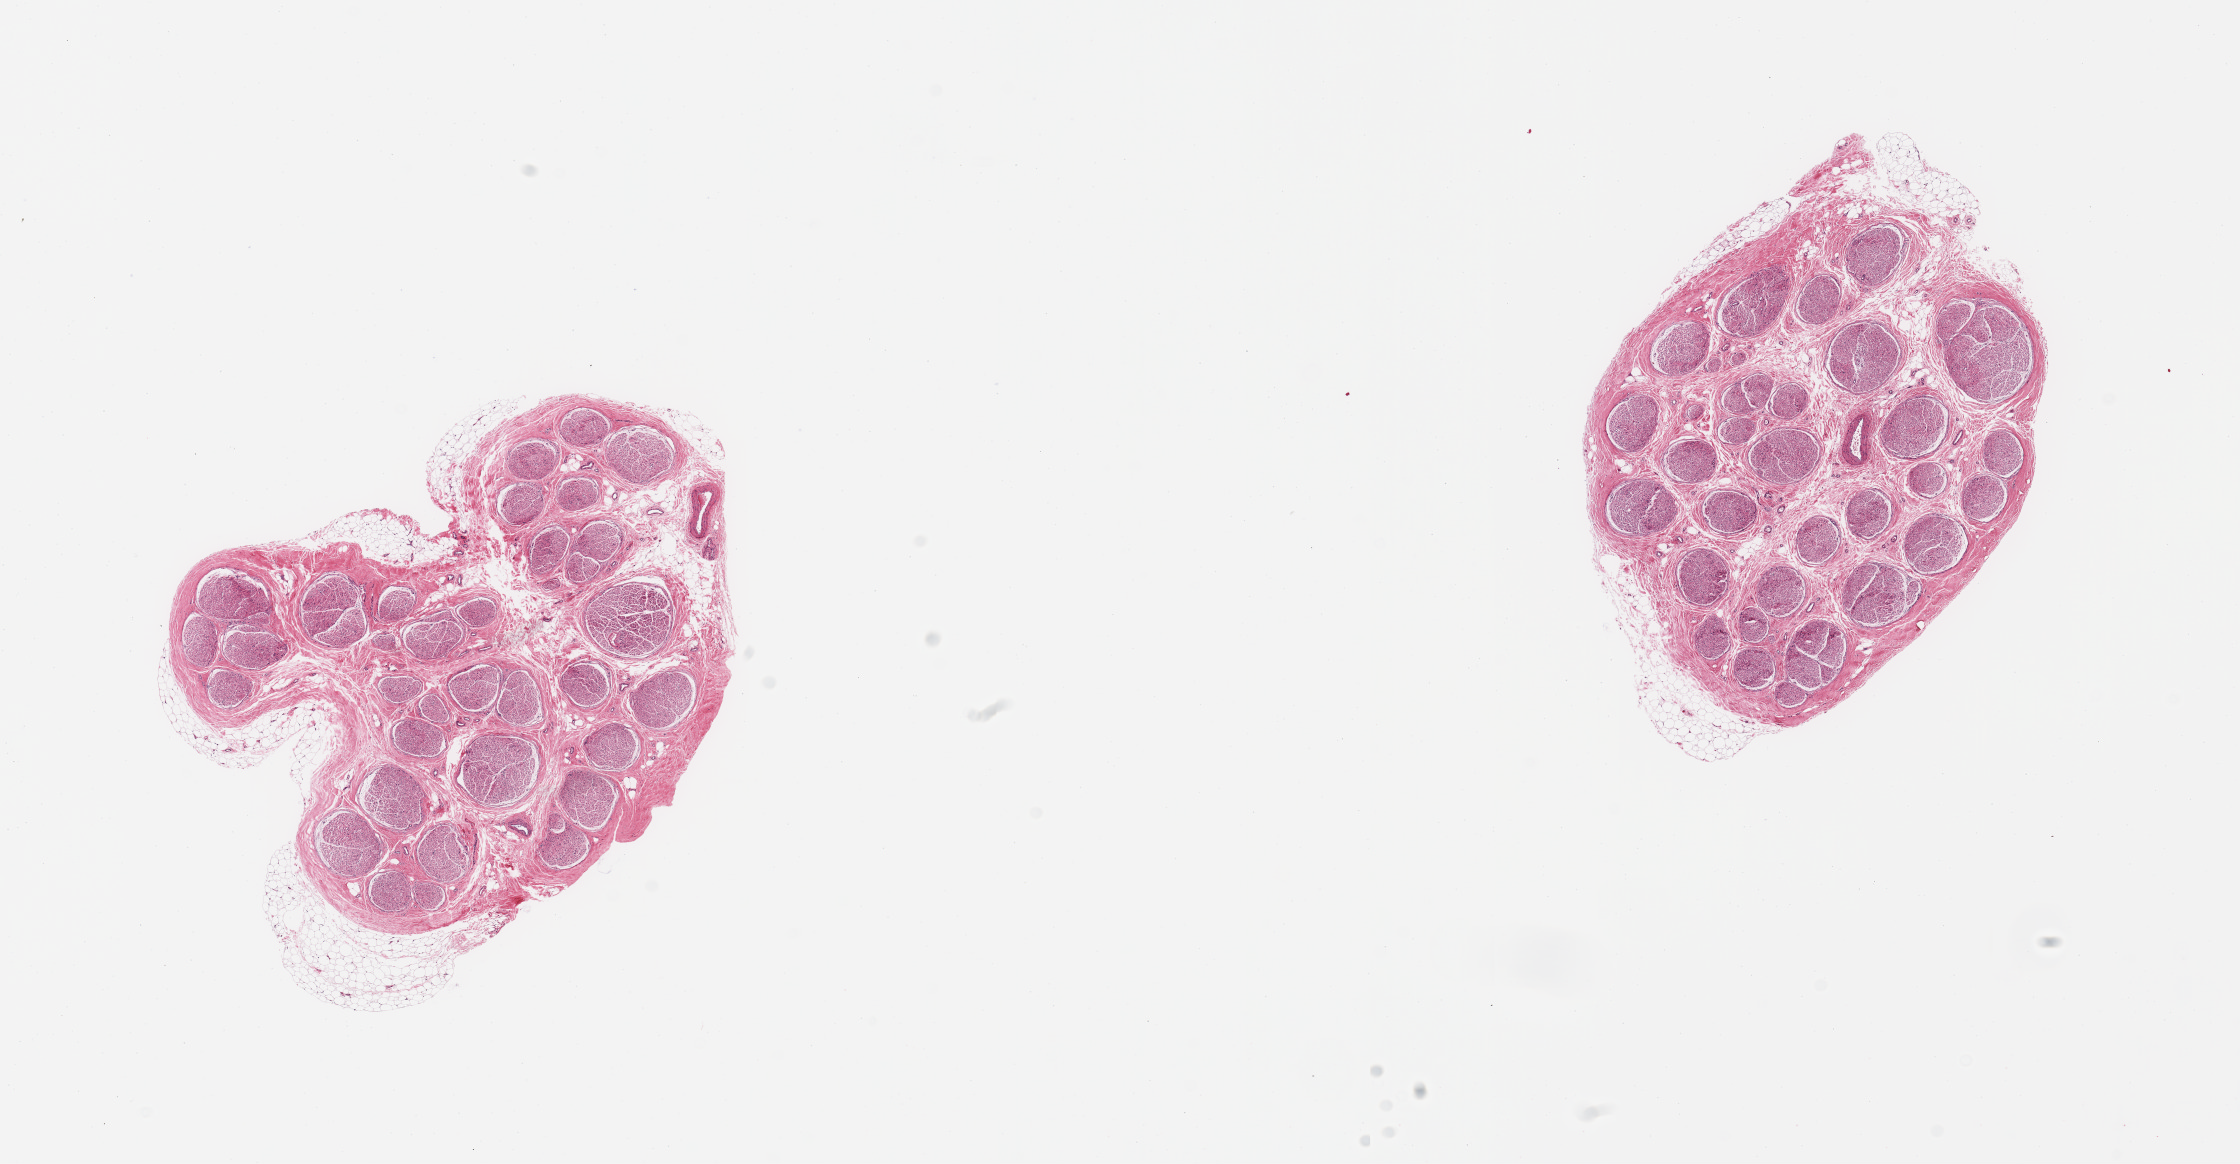
Haematoxylin and eosin whole-slide image, low-resolution overview of the scanned area, about 17.7 x 9.2 mm; PAXgene-fixed, paraffin-embedded tissue; target tissue: tibial nerve; tissue donor sample. Donor sex: female.
Pathologist's review note for this sample: 2 pieces; 10% external fat on 1 piece.